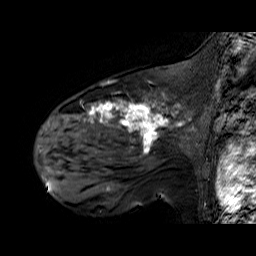
Breast MRI (dynamic contrast-enhanced), one sagittal slice. Slice 42 of 60 in the series (ordered by position). Dynamic contrast-enhanced series, time point 2 of 6 at this slice position (early post-contrast). 1.5 T. TE 6.3 ms, TR 32.9 ms. 4 mm slice thickness. 256 × 256 image matrix, field of view 200 × 200 mm. Female patient. Case-level facts recorded for this patient, not image findings: setting: breast cancer imaged before/during neoadjuvant chemotherapy; receptor status: HER2-positive.
Annotated regions visible in this slice (semi-automatically segmented with operator editing):
- analysis volume of interest (the breast-tissue region the enhancement analysis was run in; not a lesion): box from (x=48, y=92) to (x=195, y=174) px
- tumour enhancement mask (voxels above the 100 % enhancement threshold inside the analysis volume of interest): (x=64, y=93)–(x=169, y=151)